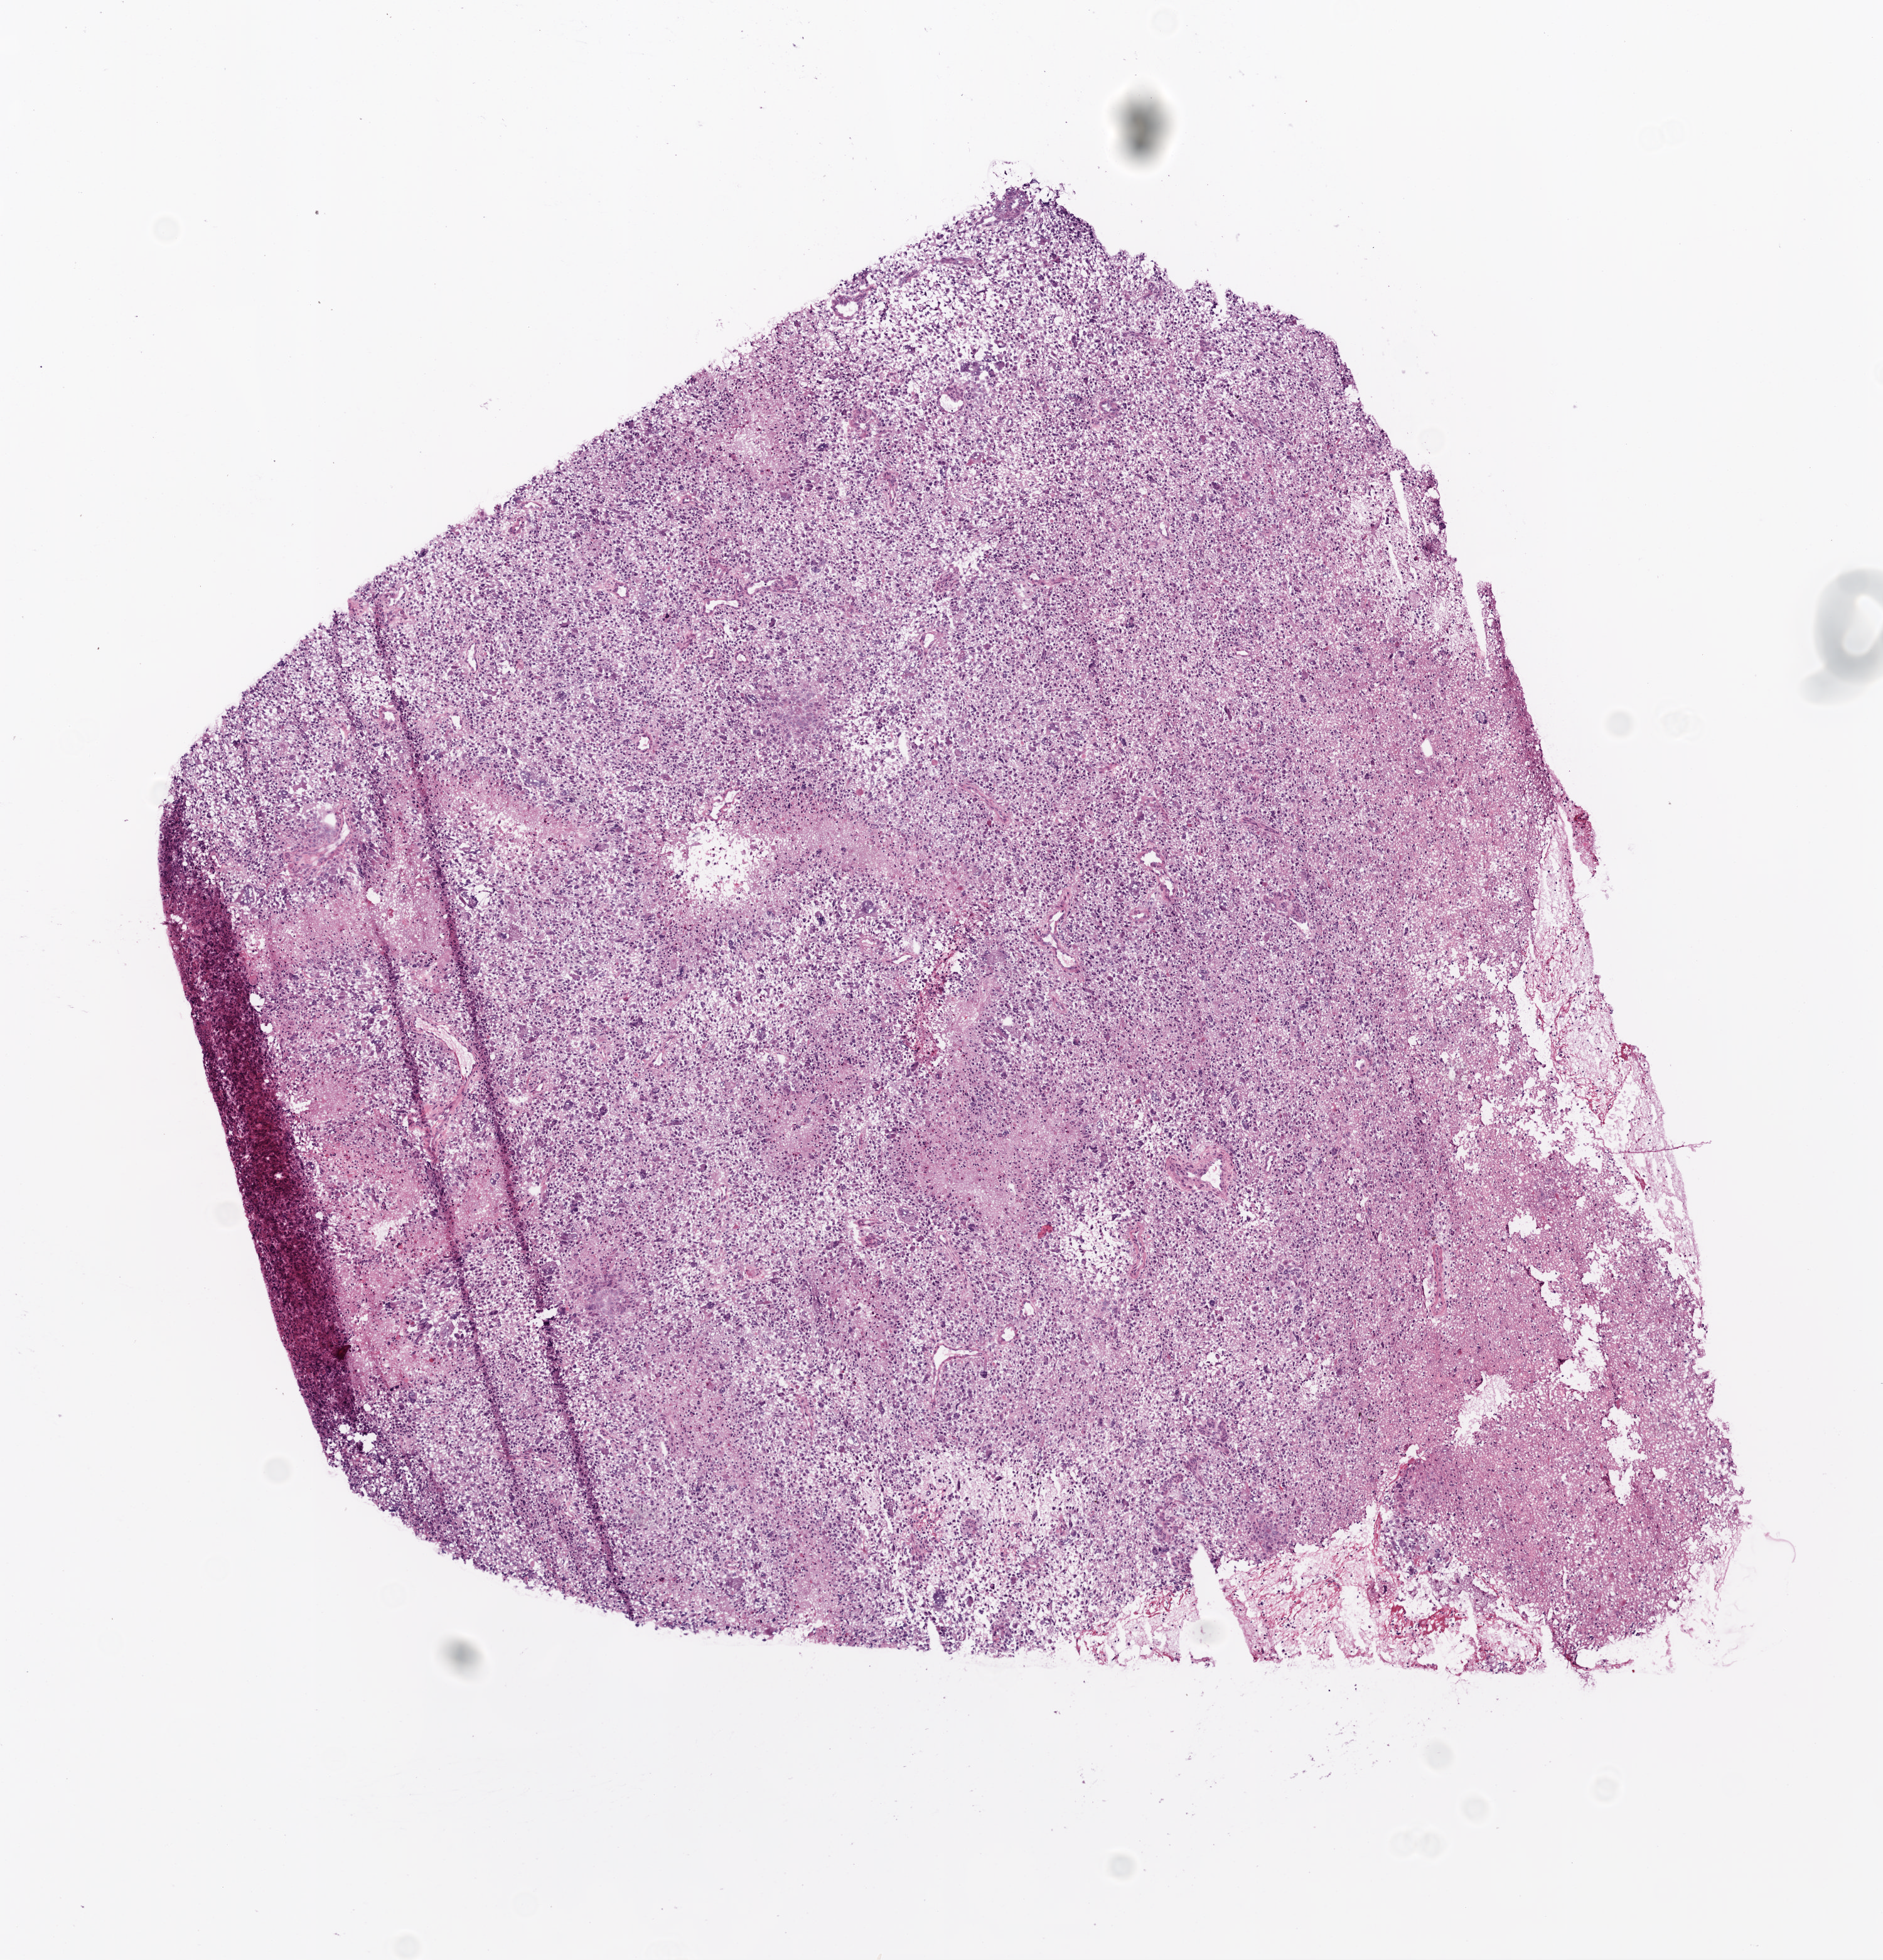
Digitized H&E-stained tissue section (whole slide) — shown as a low-resolution overview of the whole scanned area (about 6.0 x 6.3 mm), frozen section from the top of the tissue portion, sample: primary tumour, brain. Patient: female, age at initial diagnosis 48 years. Composition of this section per pathologist review: tumour cells 90%, tumour nuclei 85%, normal cells 0%, stromal cells 0%, necrosis 10%.
* pathologic diagnosis: Glioblastoma